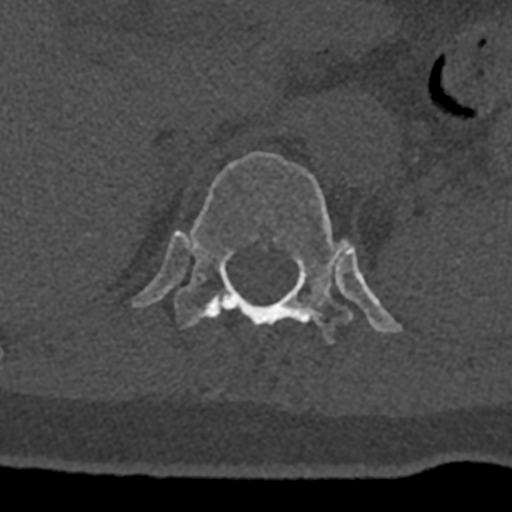
CT including the spine, one axial slice; position 499 of 797 along the scan axis; reconstruction kernel Br40s/3; bone window (W 1800 / L 400 HU); 0.5 mm slice thickness; 512 × 512 image matrix, field of view 160 × 160 mm. Patient: male, 74 years. Case-level facts recorded for this patient, not image findings: primary cancer: renal; vertebrae with lytic lesions (as recorded): T10, L1, L2, L3, L4, L5.
Structures marked on this image (semi-automatically segmented with operator editing):
- T12 vertebra: bounding box <132,151,402,344> (left, top, right, bottom; pixels)